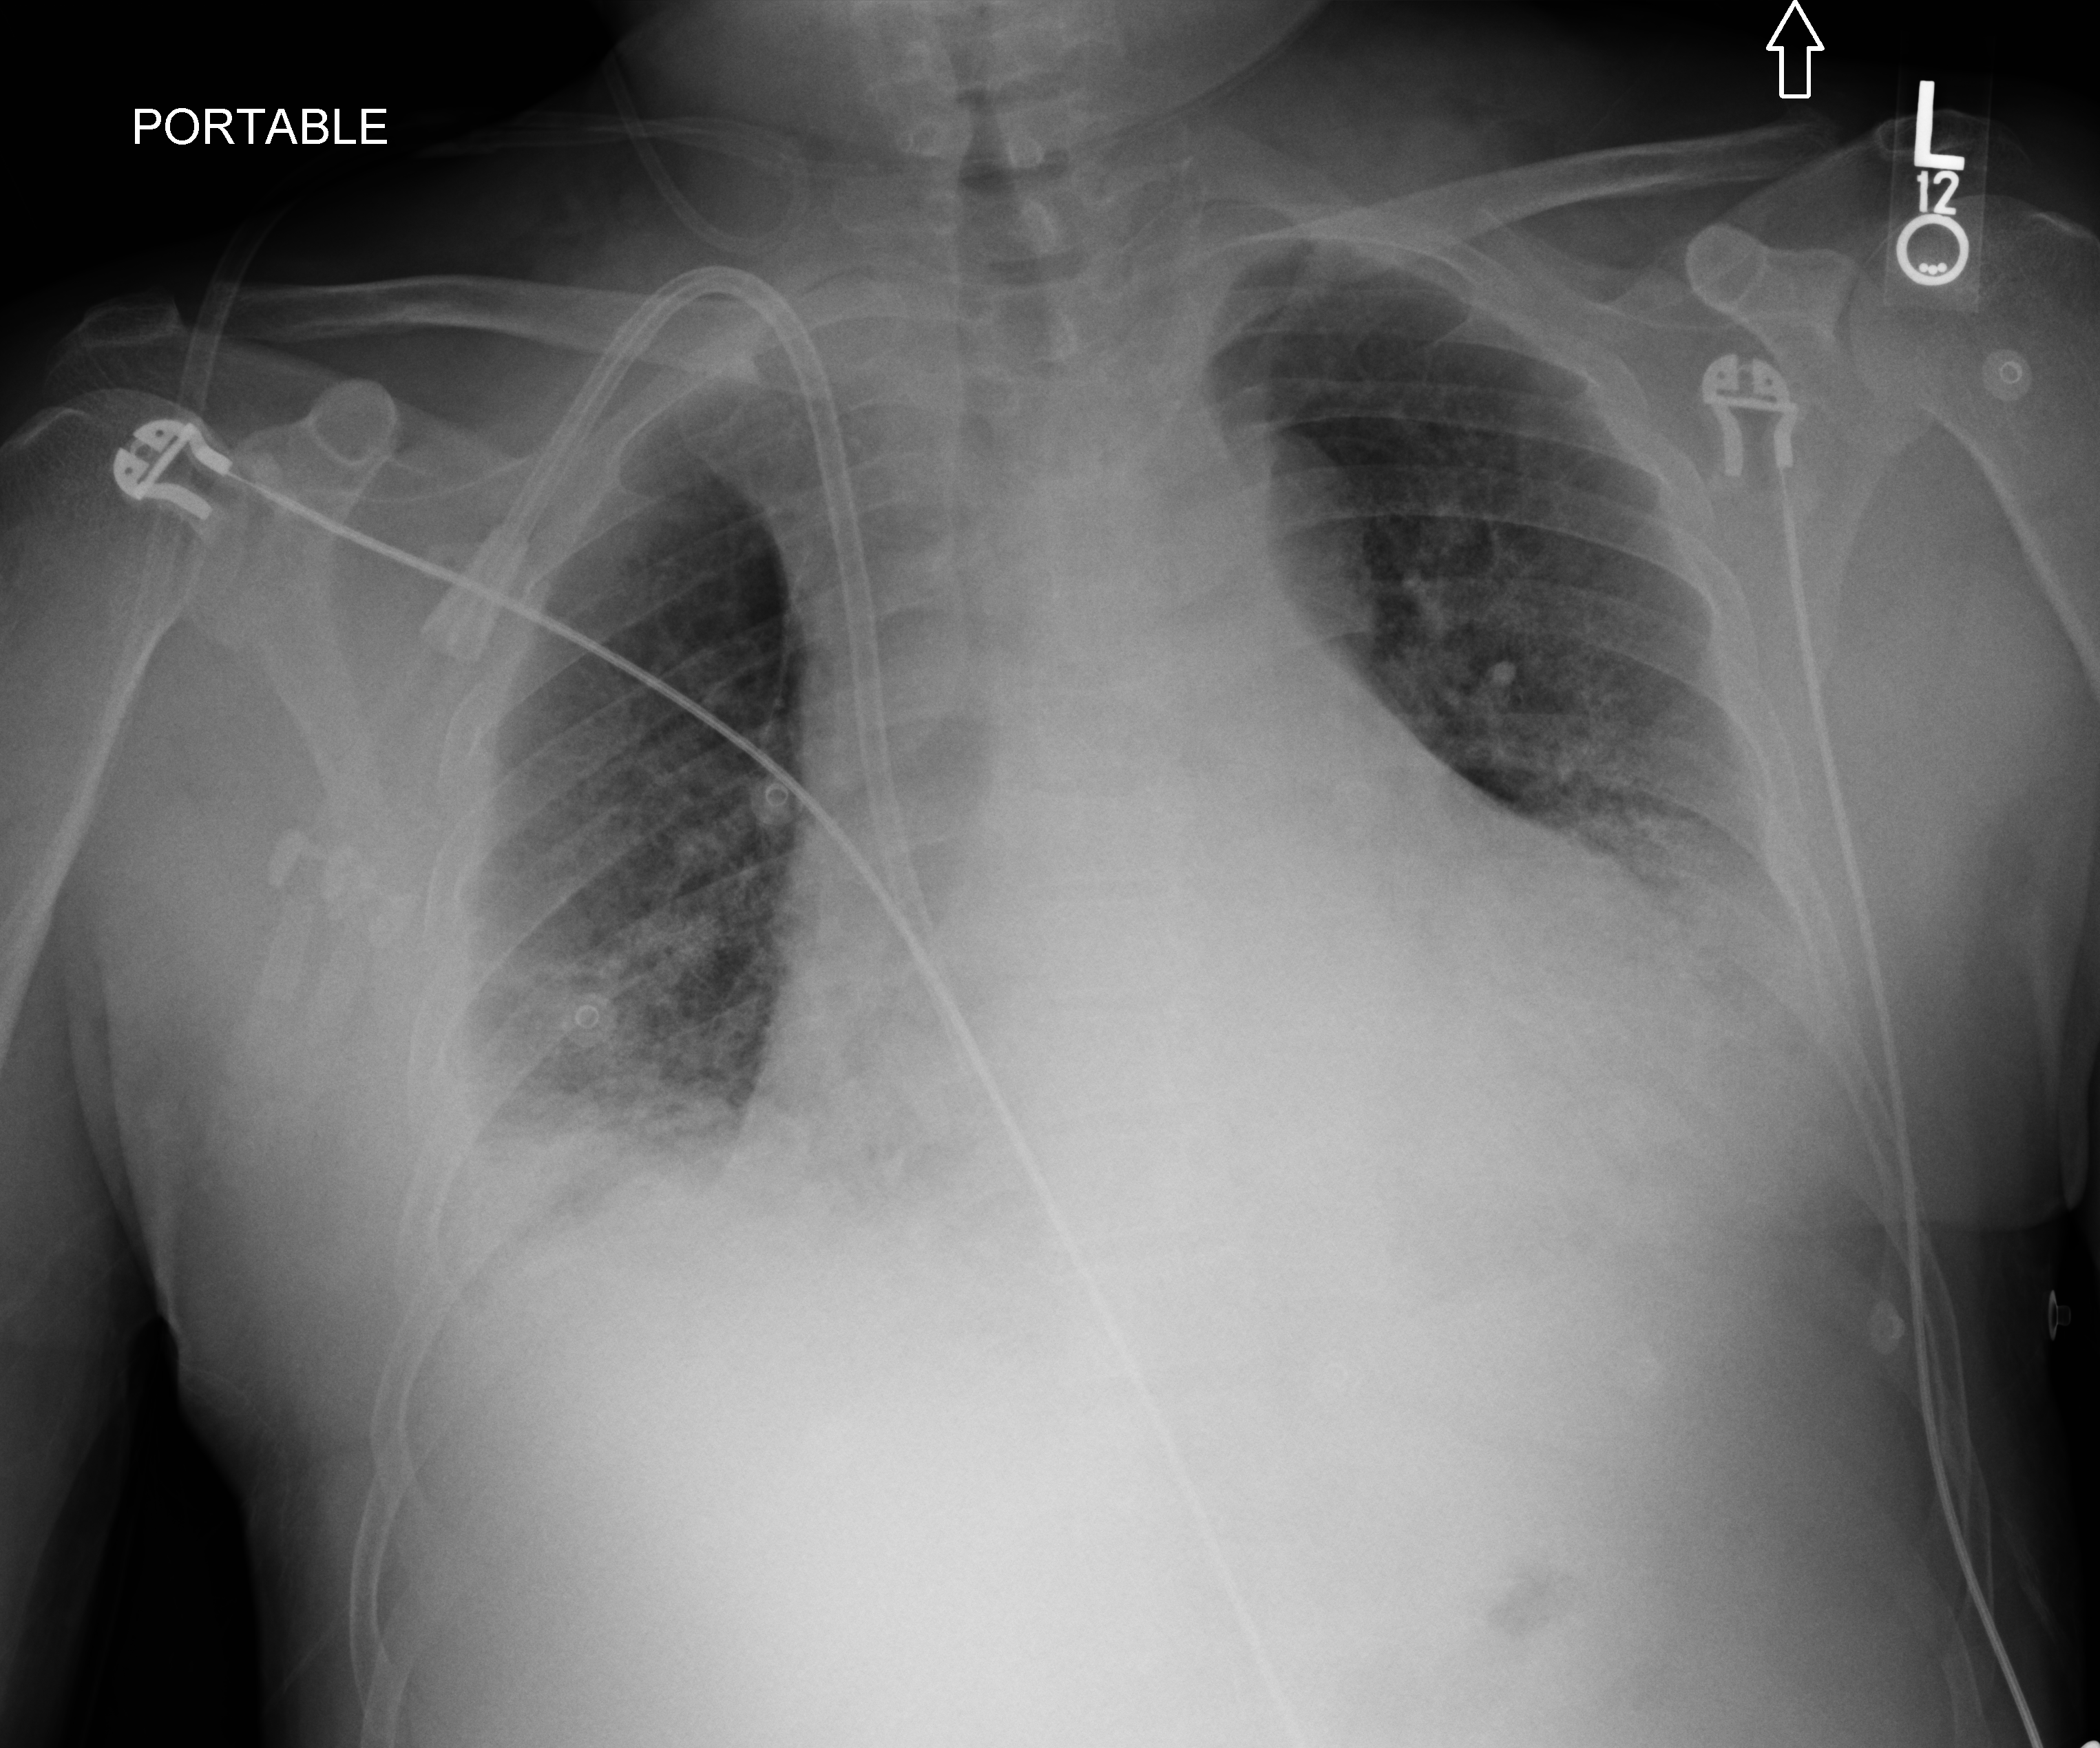
Portable chest radiograph; anteroposterior (AP) projection. Patient hospitalised with COVID-19; male, aged 18–59 years.
Admission-level facts for this patient (not findings on this image; timing relative to this image not recorded): mechanically ventilated during this hospital stay: no.